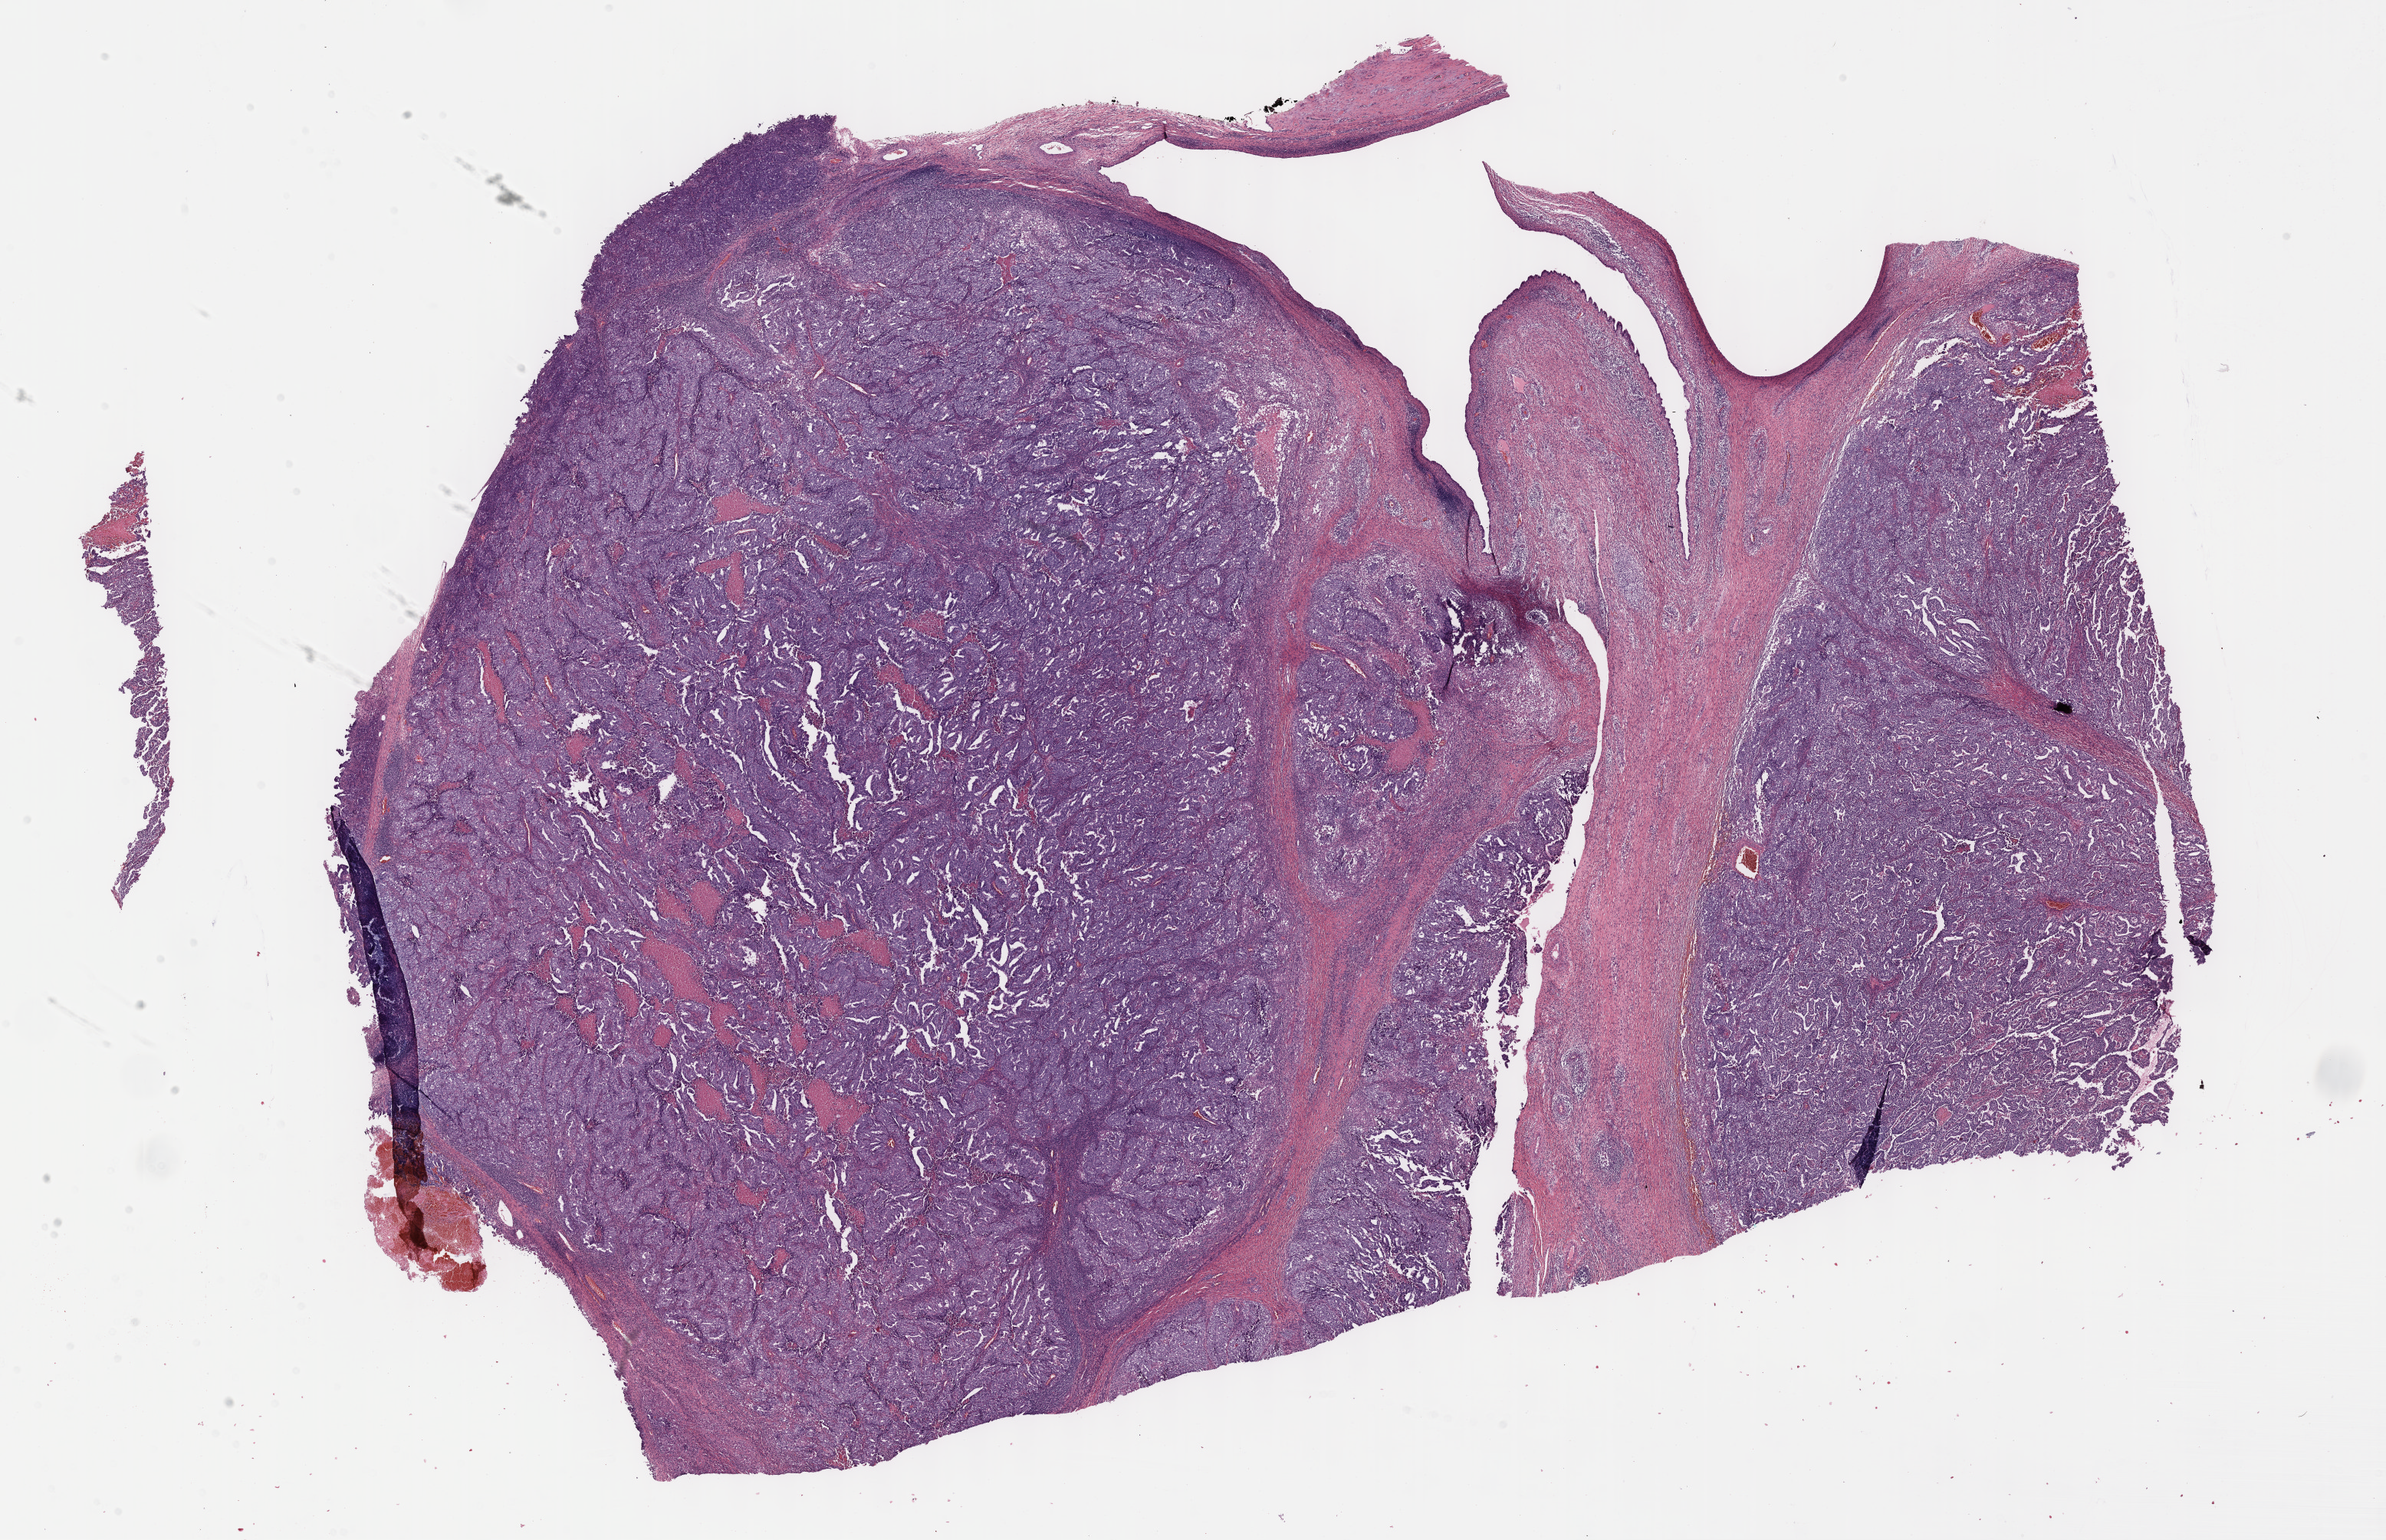
Digitized Hematoxylin and eosin (H&E) stained tissue section (whole slide) — low-resolution overview of the scanned area, about 25.2 x 16.2 mm (slide scanned at 40x); formalin-fixed paraffin-embedded (FFPE) diagnostic section; sample: primary tumour, testis. Male, age 25 years at initial diagnosis.
Histologic diagnosis: Embryonal carcinoma, NOS.